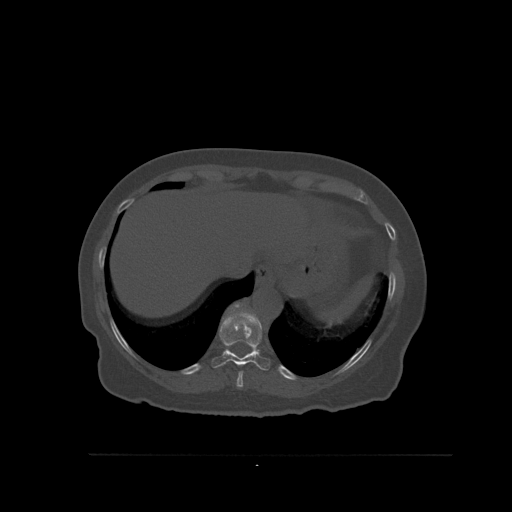
CT including the spine, one axial slice; position 320 of 527 along the scan axis; bone window (W 1800 / L 400 HU); 1.5 mm slice thickness; 512 × 512 image matrix, field of view 470 × 470 mm. Patient: female, 73 years. Case-level facts recorded for this patient, not image findings: primary cancer: breast.
Outlined on this slice (semi-automatically segmented with operator editing):
- T10 vertebra: bounding box (x1, y1, x2, y2) in pixels: (211, 313, 271, 371)
- T9 vertebra: (236, 371, 244, 388)